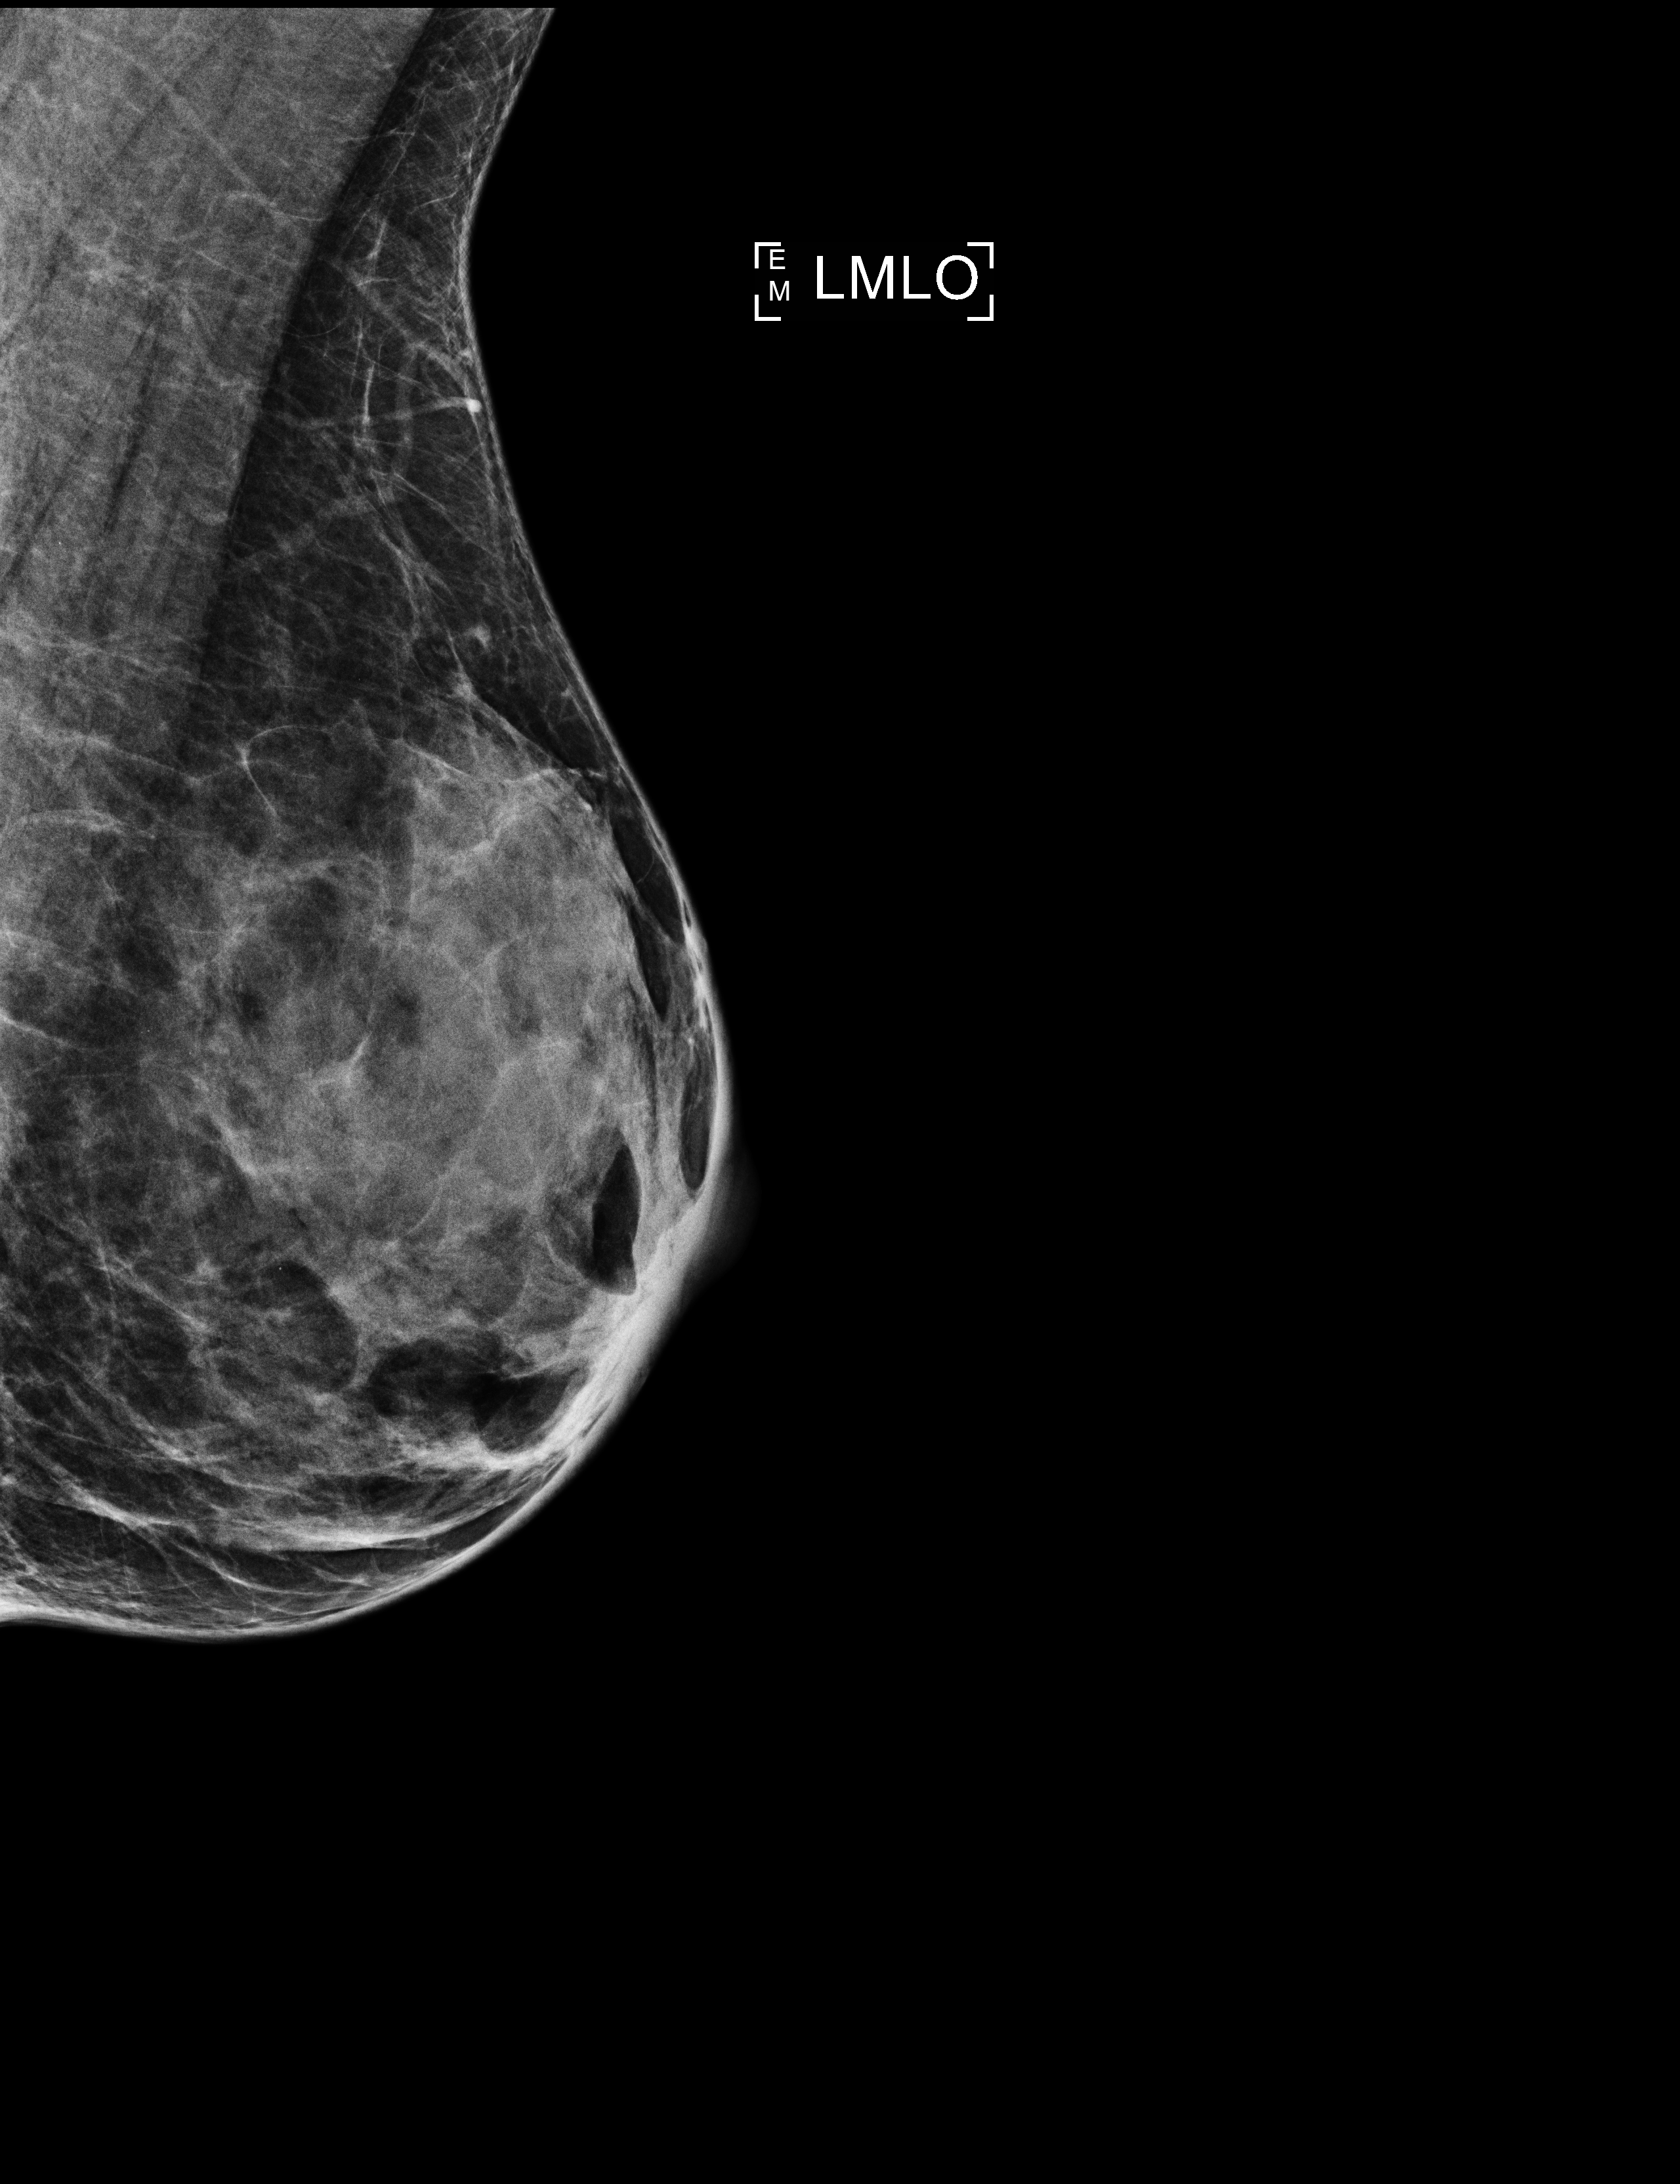
Screening examination, compressed breast thickness 32 mm. Patient: female, 65 years.
Image type: full-field digital mammogram. Breast: left. Projection: MLO view.